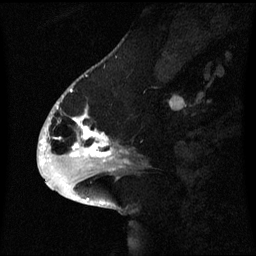
Breast MRI (dynamic contrast-enhanced), one sagittal slice; position 24 of 60 along the scan axis; dynamic contrast-enhanced series, image 2 of 3 at this slice position (ordered by acquisition); 1.5 T; TE 4.2 ms, TR 8.4 ms; 2.1 mm slice thickness; 256 × 256 image matrix, field of view 220 × 220 mm. Patient: female, 53 years. Case-level facts recorded for this patient, not image findings: setting: breast cancer imaged before/during neoadjuvant chemotherapy; receptor status: HR-positive, HER2-negative.
Structures marked on this image (semi-automatically segmented with operator editing):
- analysis volume of interest (the breast-tissue region the enhancement analysis was run in; not a lesion): bounding box <52,90,131,171> (left, top, right, bottom; pixels)
- tumour enhancement mask (voxels above the 70 % enhancement threshold inside the analysis volume of interest): <56,104,113,161>